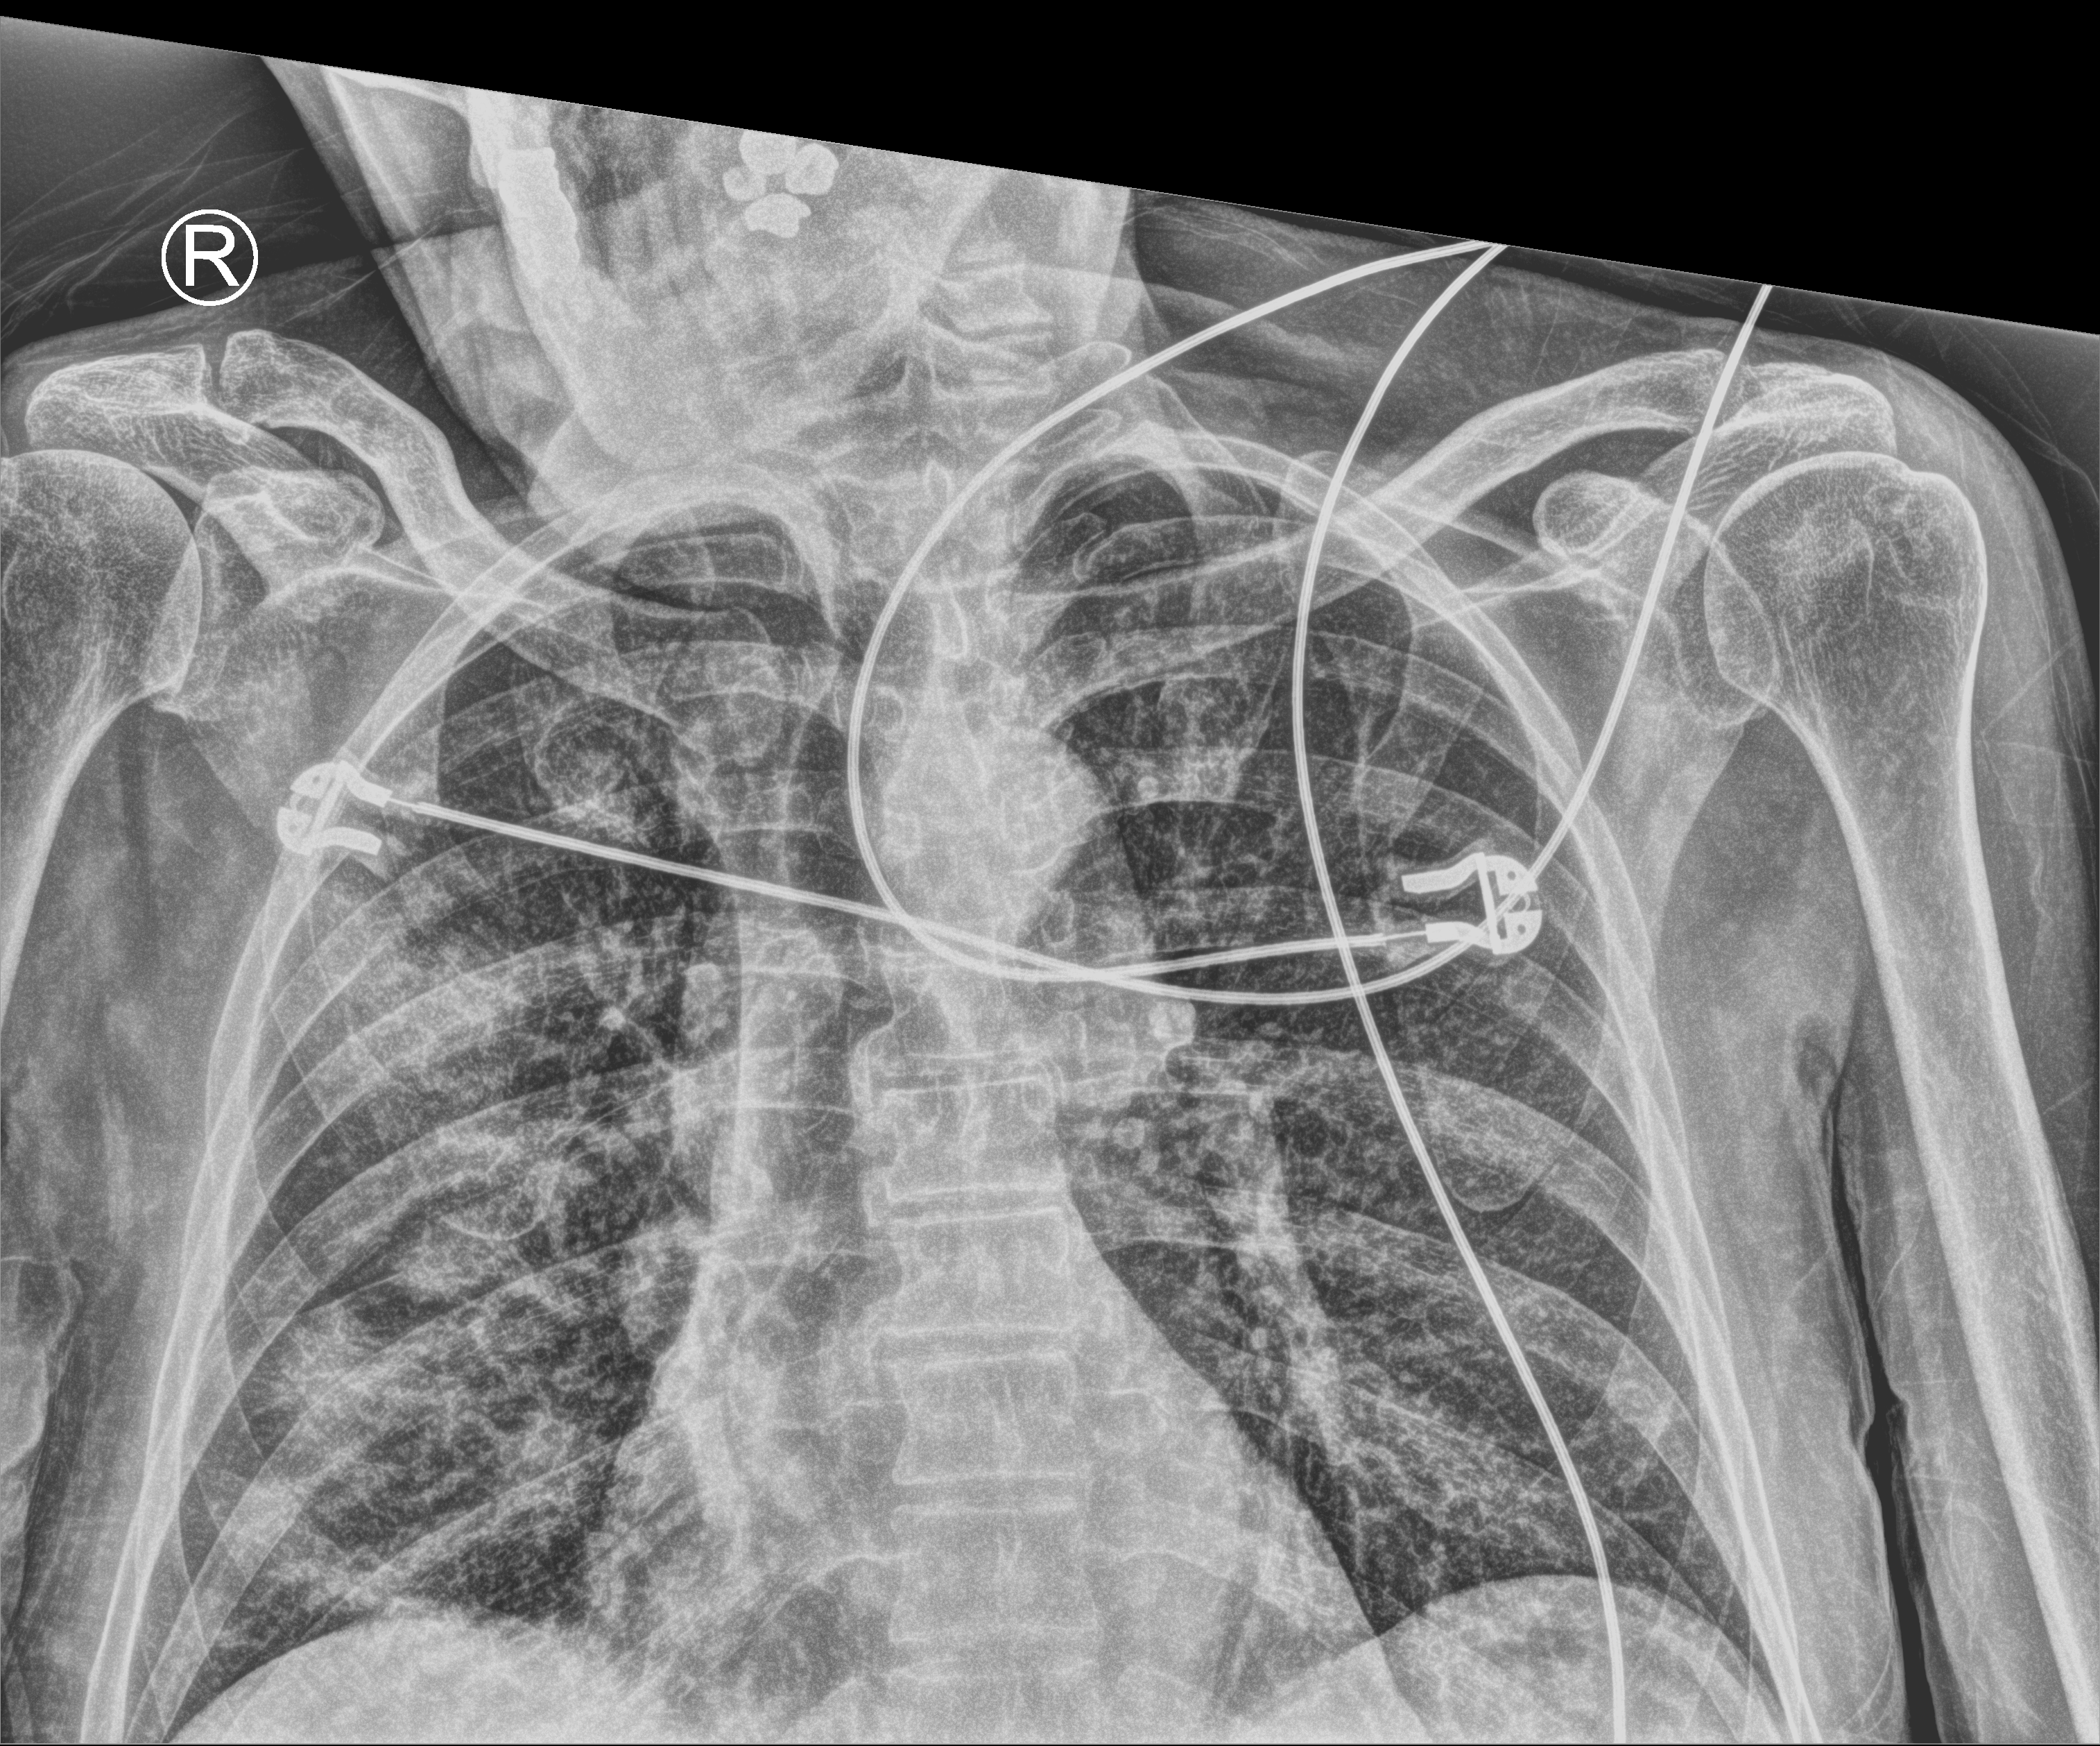
Chest X-ray (portable). Patient hospitalised with COVID-19; male, aged 60–74 years.
Admission-level facts for this patient (not findings on this image; timing relative to this image not recorded): mechanically ventilated during this hospital stay: no; length of hospital stay: 7 days.